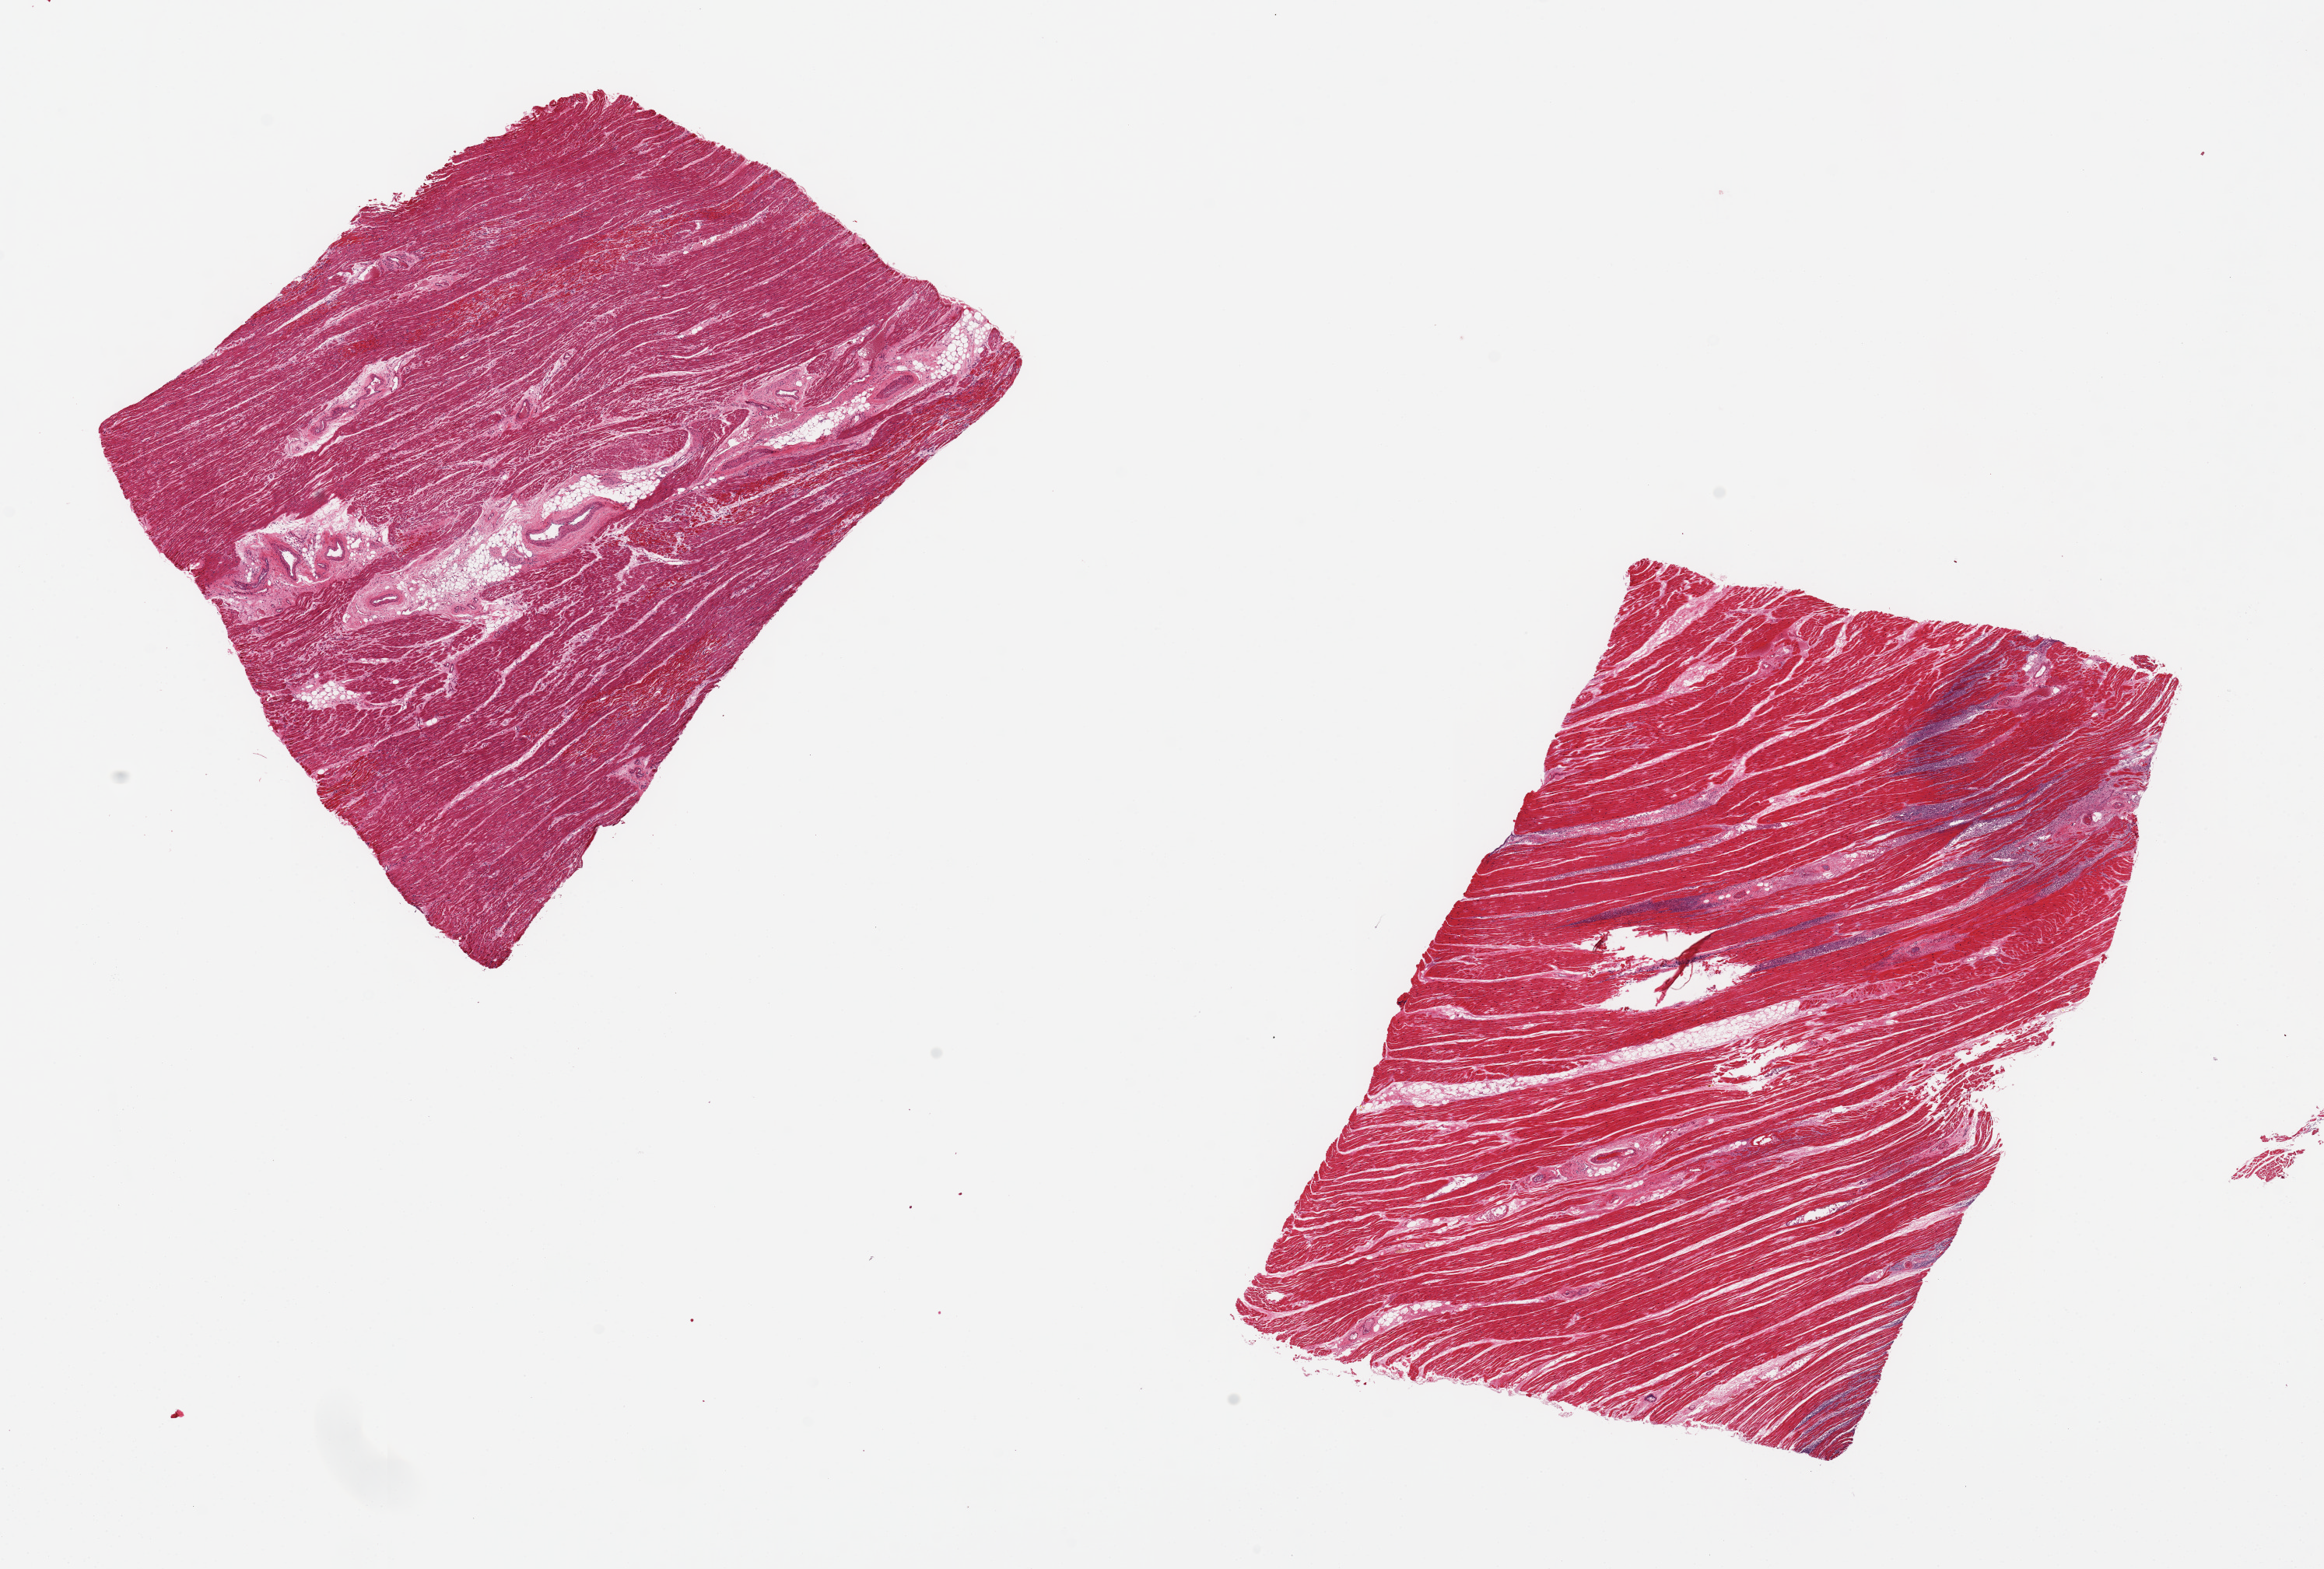
Whole-slide image, hematoxylin and eosin (H&E) stain — whole scanned area (about 23.6 x 16.0 mm) shown as a low-resolution overview, PAXgene-fixed paraffin-embedded (PFPE) section, section of heart (target tissue), donor tissue sample. Donor: male.
Review note (as recorded): 2 ~8x6mm pieces. Prominent acute infarct with polys/edema.